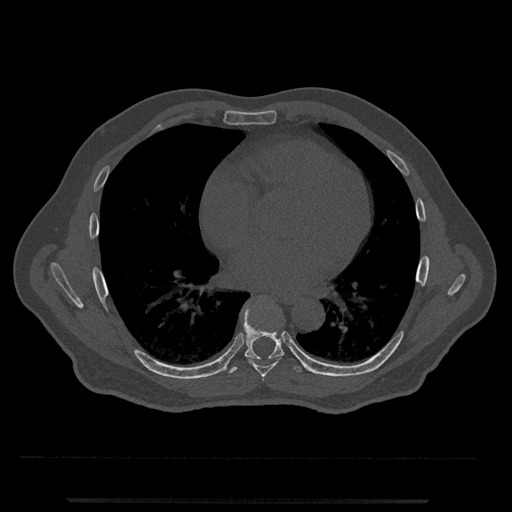
CT including the spine, one axial slice. Slice 655 of 797 in the series (ordered by position). Reconstruction kernel Br40s/3. Bone window (W 1800 / L 400 HU). 512 × 512 image matrix. Patient: male, 63 years. Case-level facts recorded for this patient, not image findings: primary cancer: prostate.
Outlined on this slice (semi-automatic segmentation, software-assisted and operator-edited):
- T7 vertebra: box from (x=247, y=356) to (x=282, y=379) px
- T8 vertebra: (x=228, y=300)–(x=302, y=374)